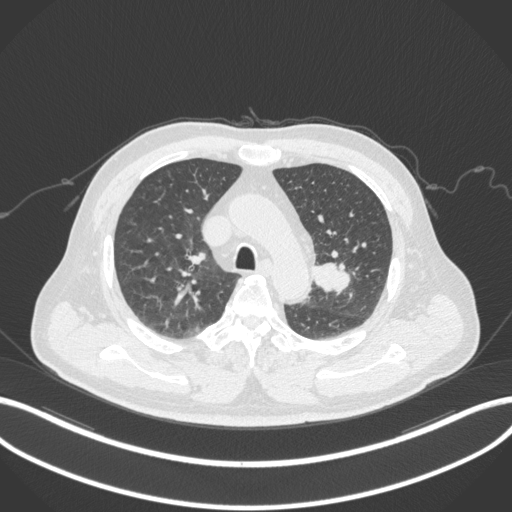
Chest CT, one axial slice; slice 214 of 286 in the series (ordered by position); reconstruction kernel B31f; 120 kVp; lung window (W 1500 / L -600 HU); 512 × 512 image matrix. Patient: male, 67 years. Case-level facts recorded for this patient, not image findings: clinical TNM (as recorded): T2a N1 M0; histopathological grade: G3.
Structures marked on this image (bounding box drawn by a radiologist):
- lung tumour (recorded histology: adenocarcinoma): bounding box (x1, y1, x2, y2) in pixels: (308, 258, 352, 295)